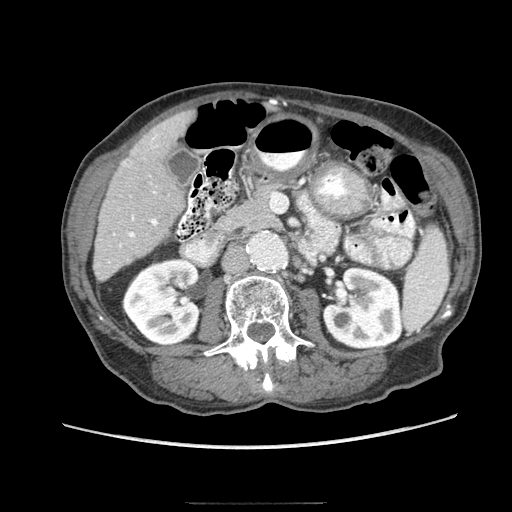
Contrast-enhanced abdominal CT (liver protocol), one axial slice; reconstruction kernel STANDARD; 140 kVp; soft-tissue window (W 400 / L 40 HU); 512 × 512 image matrix, field of view 360 × 360 mm. Case-level facts recorded for this patient, not image findings: diagnosis: hepatocellular carcinoma (patient treated with transarterial chemoembolisation; whether this scan precedes or follows treatment is not stated here); TNM stage (as recorded): Stage-I; Child-Pugh class: A; tumour differentiation: moderately differentiated; tumour nodularity: uninodular.
Annotated regions visible in this slice (semi-automatic segmentation, software-assisted and operator-edited):
- liver parenchyma outside the tumour (the mass and vessels are separate outlines, so this box may not span the whole liver): bounding box [x1, y1, x2, y2] px = [92, 110, 196, 280]
- liver vessels: [119, 137, 158, 247]